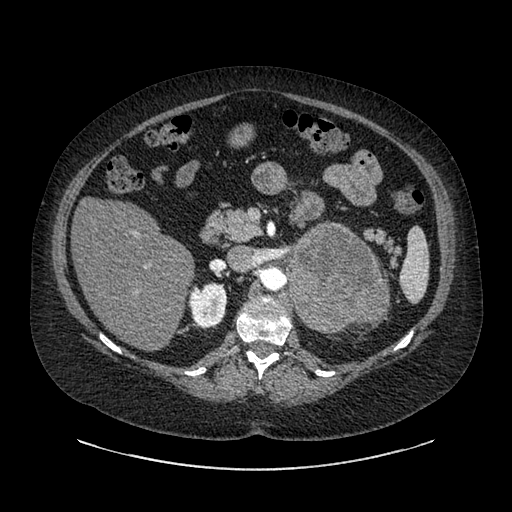
Contrast-enhanced abdominal CT, one axial slice. Slice 546 of 769 in the series (ordered by position). Reconstruction kernel SOFT. 120 kVp. Intravenous contrast given. Soft-tissue window (W 400 / L 40 HU). 0.62 mm slice thickness. 512 × 512 image matrix. Patient: female, 61 years. Case-level facts recorded for this patient, not image findings: diagnosis: adrenocortical carcinoma; tumour side: left adrenal; tumour size at pathology: 13 cm; Ki-67 index: 79 %; stage (as recorded): 2.
Annotated regions visible in this slice (semi-automatic segmentation, software-assisted and operator-edited):
- mass: bounding box (x1, y1, x2, y2) in pixels: (291, 226, 385, 332)